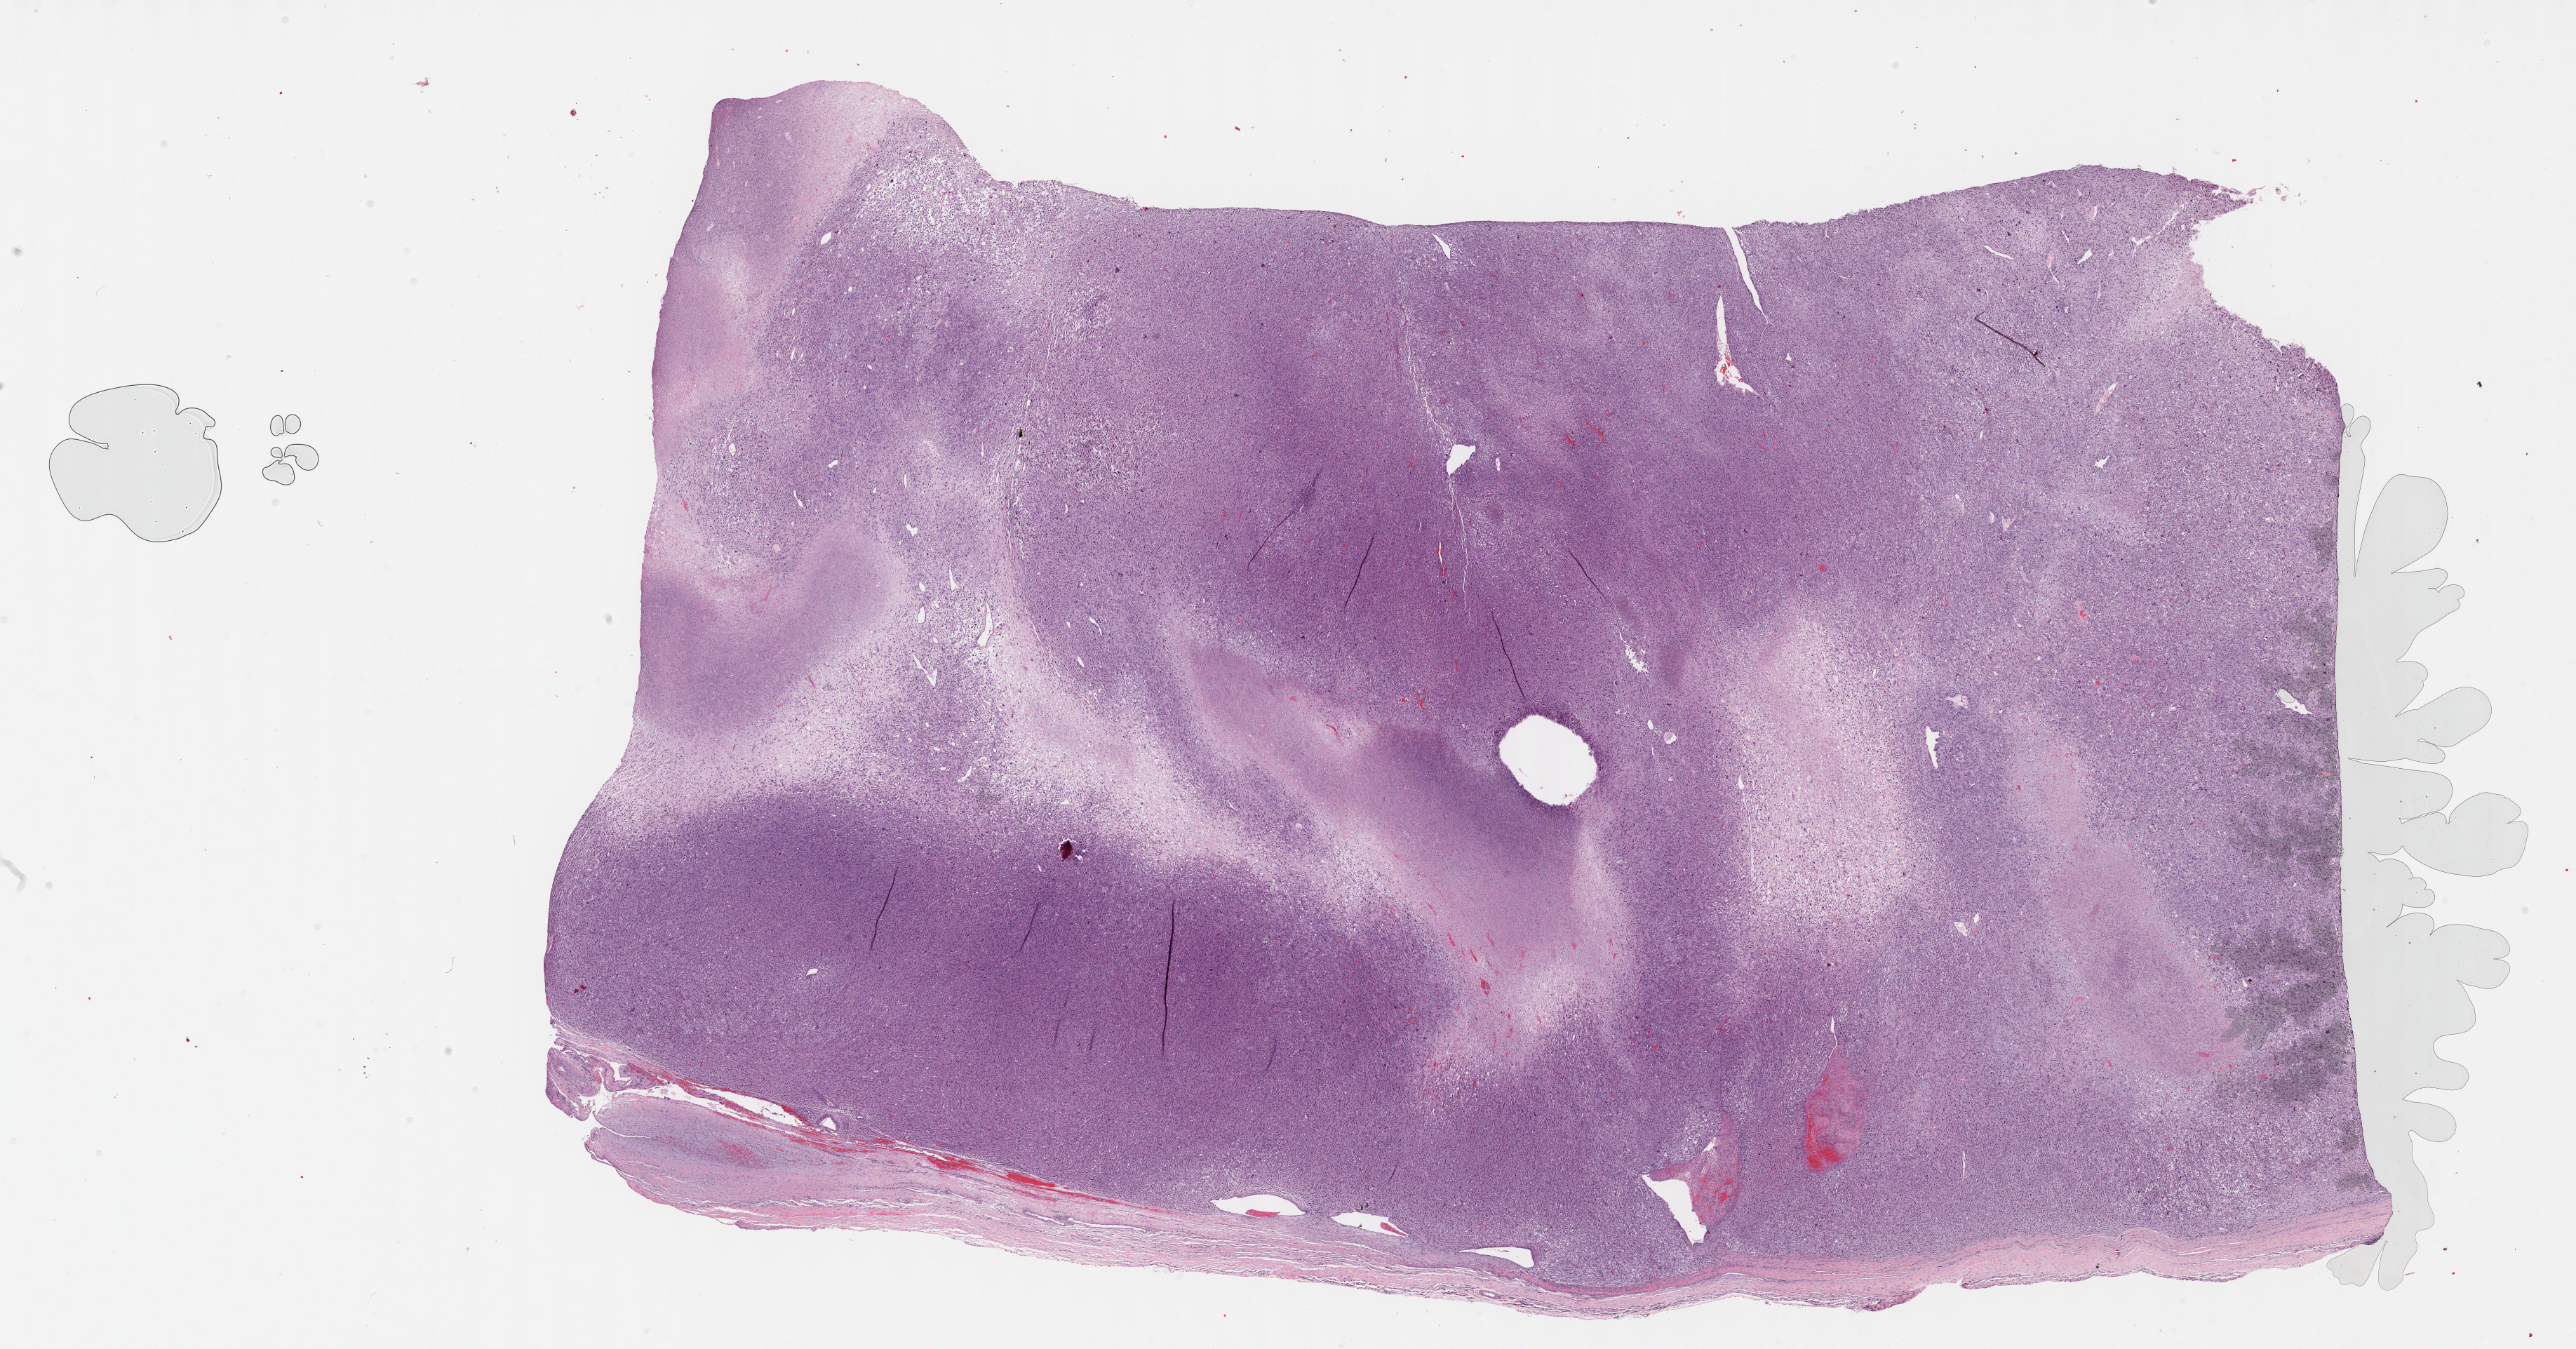
H&E whole-slide image, low-resolution overview of the scanned area, about 29.7 x 15.5 mm; formalin-fixed paraffin-embedded (FFPE) diagnostic section; primary tumour sample from the connective, subcutaneous and other soft tissues. Male, age 60 years at initial diagnosis.
Pathologic diagnosis: Undifferentiated sarcoma (connective, subcutaneous and other soft tissues of lower limb and hip).